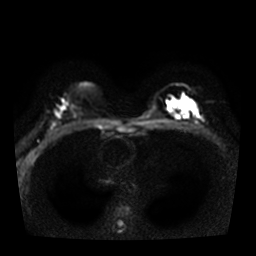
Breast MRI, one axial slice. Slice 20 of 36 in the series (ordered by position). Diffusion-weighted series; image 2 of 4 stored at this slice position (different b-values; order by instance number). 3 T. 5 mm slice thickness. 256 × 256 image matrix. Female patient.
Structures marked on this image (manually delineated by an expert):
- tumour on diffusion-weighted imaging: bounding box <167,95,199,116> (left, top, right, bottom; pixels)